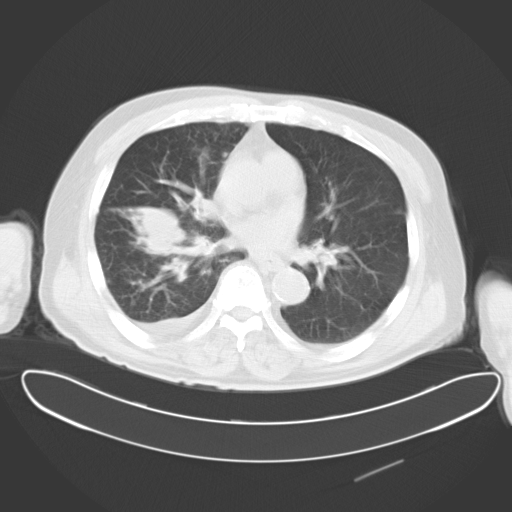
Chest CT, one axial slice; position 14 of 30 along the scan axis; reconstruction kernel B40f; 120 kVp; lung window (W 1500 / L -600 HU); 10 mm slice thickness; 512 × 512 image matrix, field of view 427 × 427 mm. Patient: male, 78 years. Case-level facts recorded for this patient, not image findings: clinical TNM (as recorded): T2 N1 M1.
Annotated regions visible in this slice (bounding box drawn by a radiologist):
- lung tumour (recorded histology: adenocarcinoma): bounding box (x1, y1, x2, y2) in pixels: (124, 194, 216, 271)